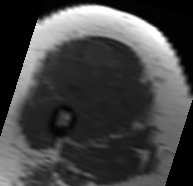
MRI of an extremity soft-tissue mass, one axial slice; slice 33 of 91 in the series (ordered by position); MR volume resampled by the dataset authors to the PET/CT grid (not the native acquisition matrix); 193 × 186 image matrix. Female patient. From the clinical record (not read from this slice): histological type: malignant solitary fibrous tumor; grade: intermediate; site of the primary tumour: right thigh.
Annotated regions visible in this slice (expert contour drawn on MRI and transferred to this co-registered scan by the dataset authors):
- gross tumour volume including surrounding oedema: bounding box (x1, y1, x2, y2) in pixels: (33, 39, 150, 130)
- gross tumour volume (mass): (40, 39, 148, 127)